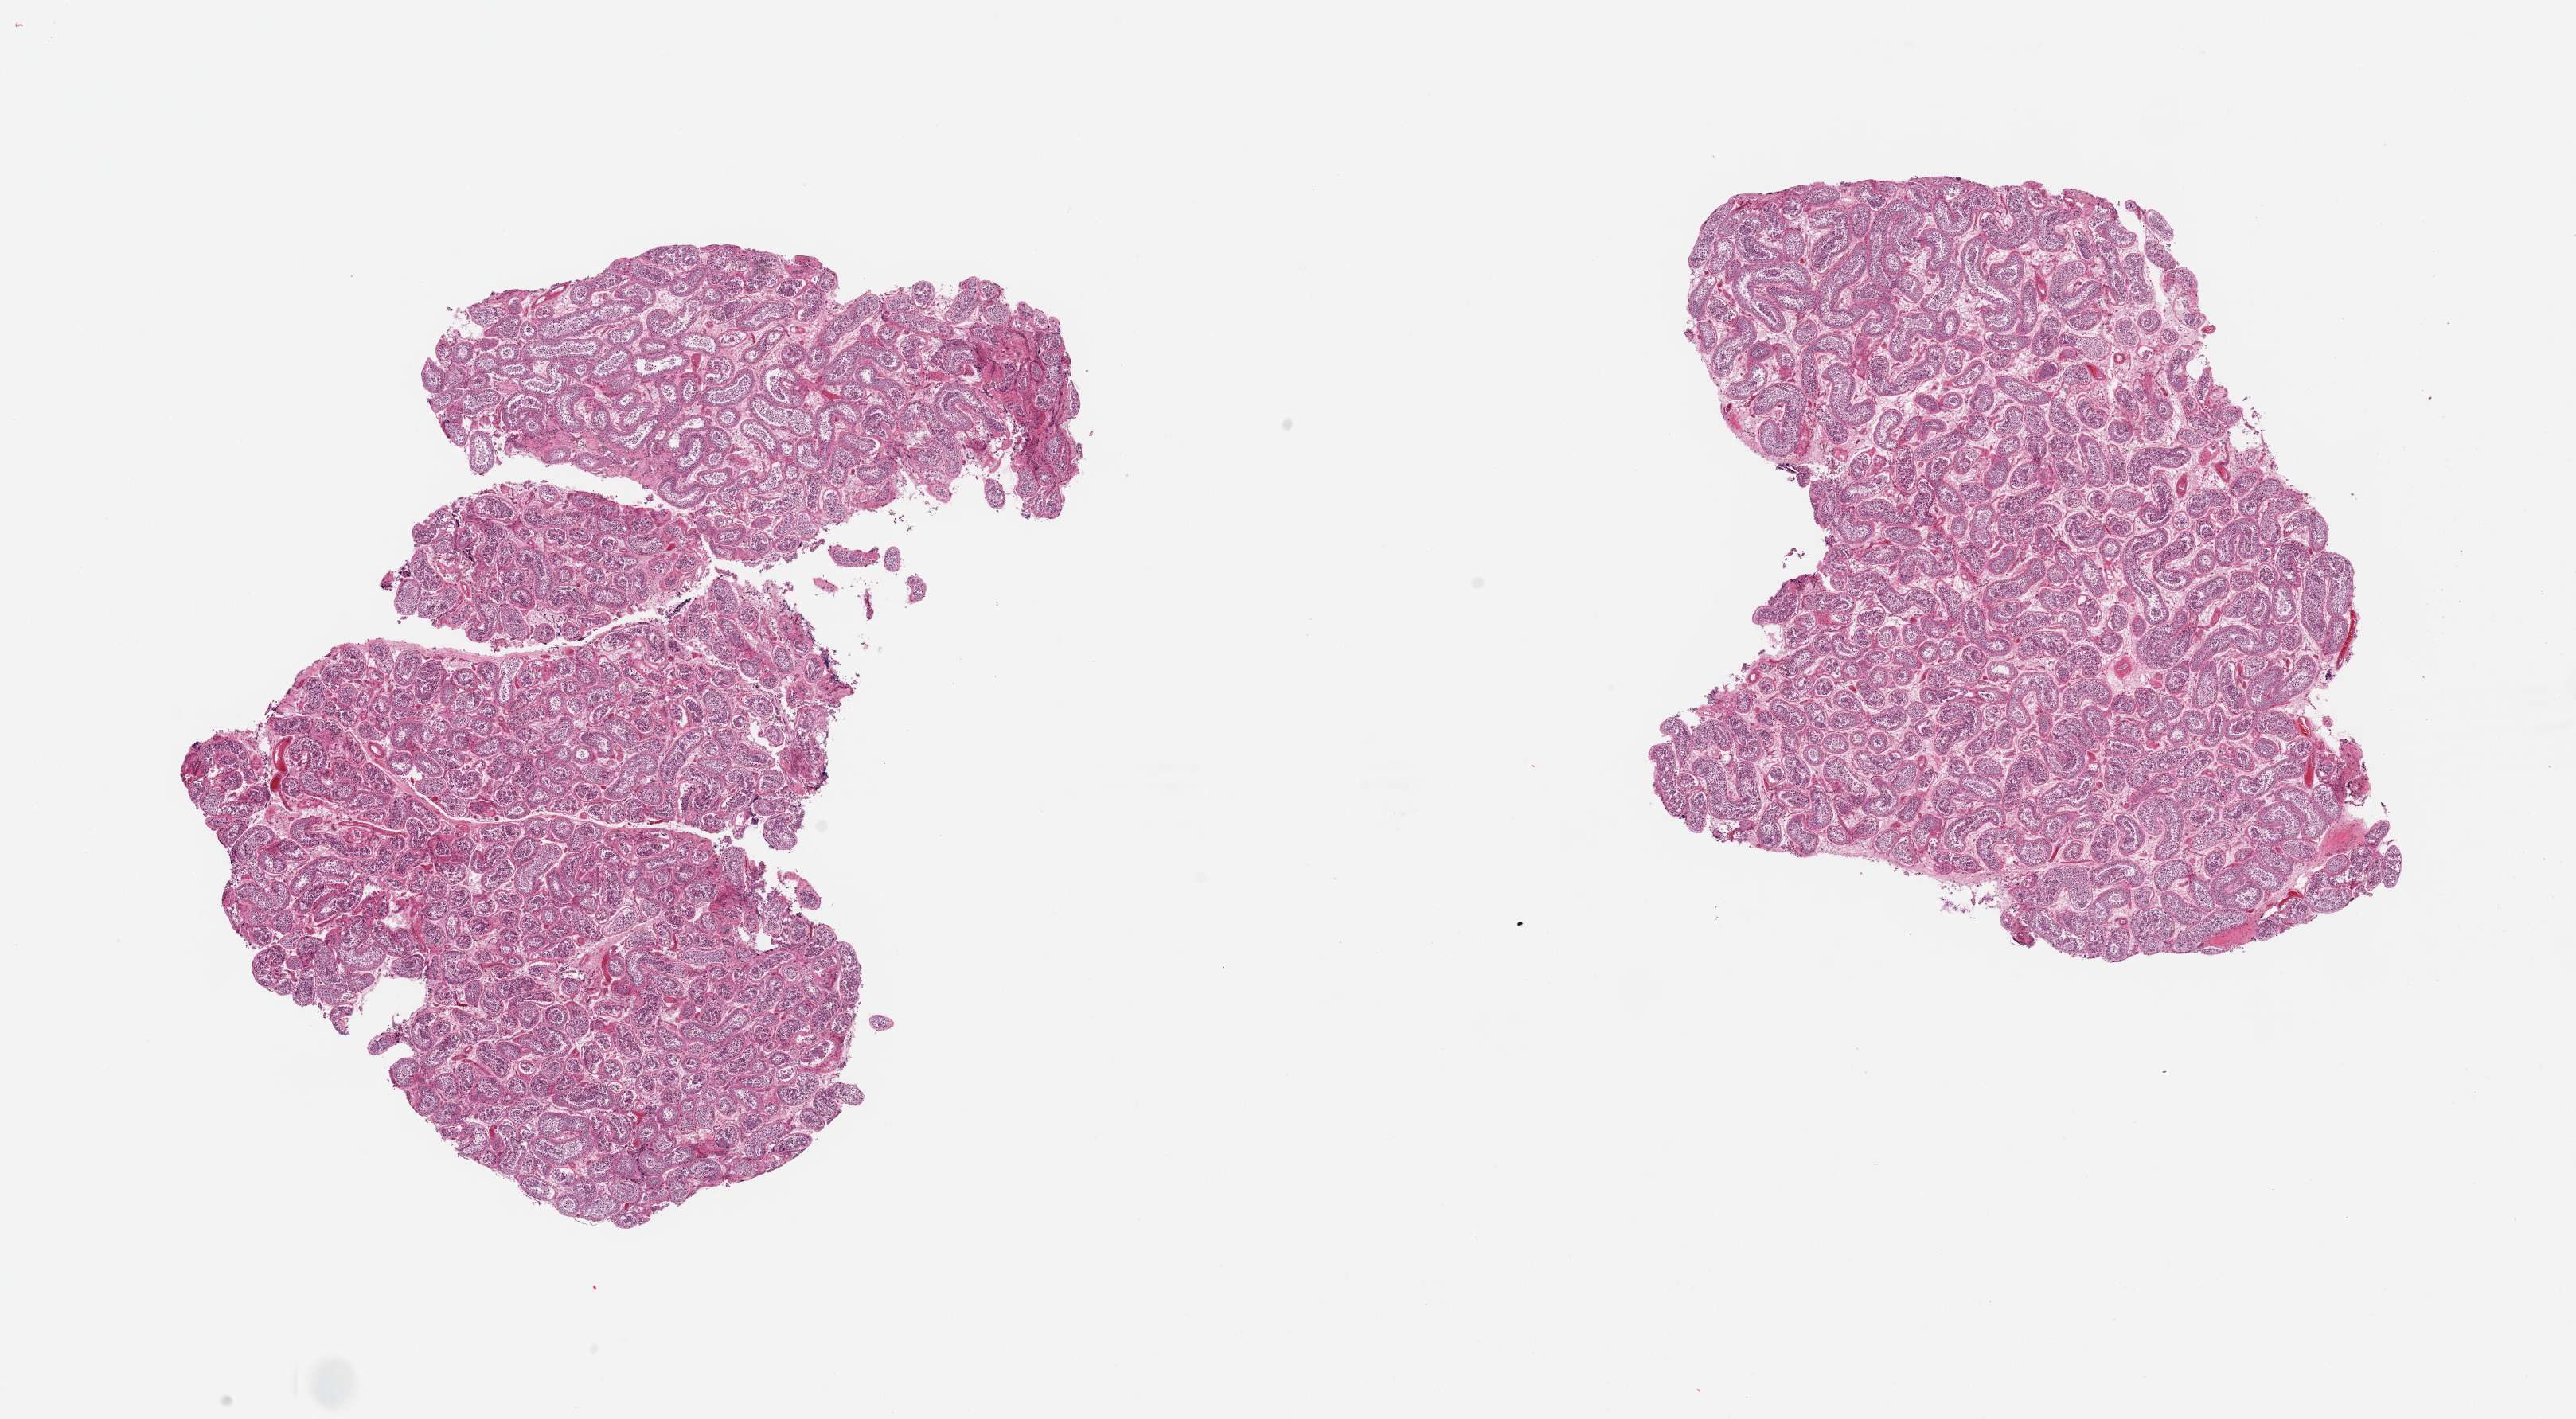
H&E whole-slide image, brightfield — shown as a low-resolution overview of the whole scanned area (about 25.6 x 14.1 mm). PAXgene-fixed, paraffin-embedded tissue. Sampled site (target tissue): testis. Donor tissue sample. Male donor.
Review note (as recorded): 2 pieces, robust spermatogenesis.